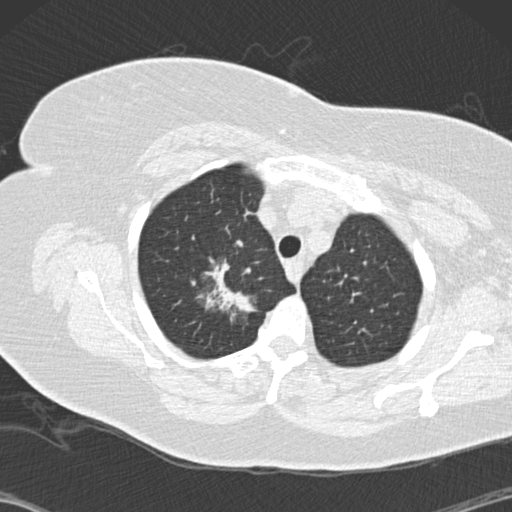
Low-dose screening chest CT, one axial slice. Position 119 of 146 along the scan axis. Lung window (W 1500 / L -600 HU). 512 × 512 image matrix, field of view 350 × 350 mm.
Structures marked on this image (outlined manually by an expert reader):
- lesion 1 (tumor, upper lobe of right lung): bounding box (x1, y1, x2, y2) in pixels: (205, 262, 255, 316)